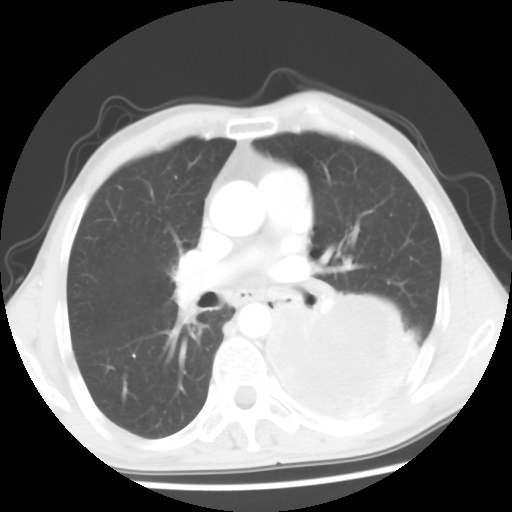
Chest CT, one axial slice. Slice 31 of 56 in the series (ordered by position). Reconstruction kernel STANDARD. 120 kVp. Lung window (W 1500 / L -600 HU). 5 mm slice thickness. 512 × 512 image matrix. Male patient, age 60 years. From the clinical record (not read from this slice): clinical TNM (as recorded): T4 N0 M0.
Outlined on this slice (bounding box drawn by a radiologist):
- lung tumour (recorded histology: squamous cell carcinoma): box from (x=249, y=286) to (x=416, y=428) px